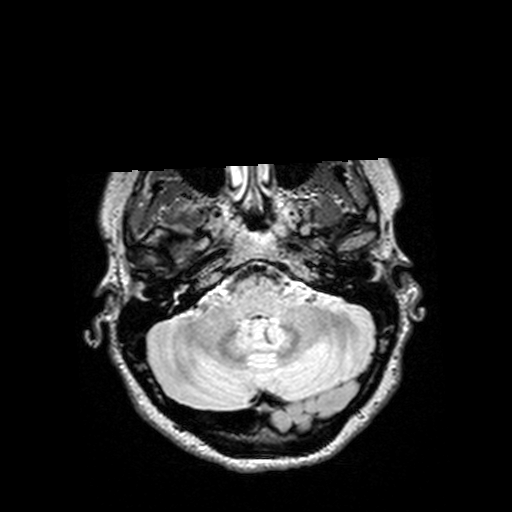
Brain MRI from a brain-tumour surgery series, one axial slice; slice 113 of 144 in the series (ordered by position); T2 FLAIR; 1 mm slice thickness; 512 × 512 image matrix. From the clinical record (not read from this slice): histopathology: Astrocytoma; WHO grade: 3; IDH mutation: yes; tumour location: Right Insular Temporal.
Outlined on this slice (expert manual segmentation):
- tumour: bounding box <163,235,197,255> (left, top, right, bottom; pixels)